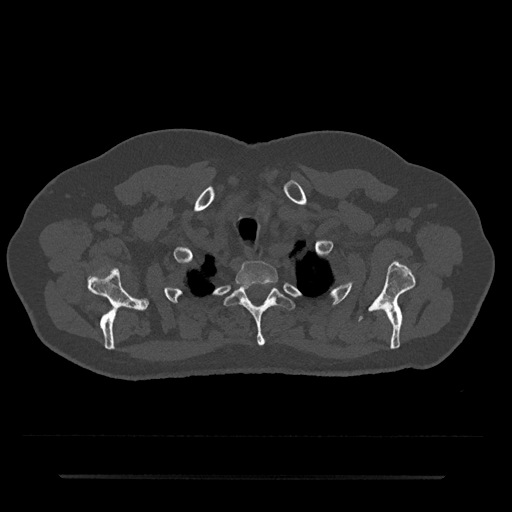
CT including the spine, one axial slice; slice 615 of 797 in the series (ordered by position); reconstruction kernel Br40s/3; 120 kVp; bone window (W 1800 / L 400 HU); 512 × 512 image matrix. Patient: male, 69 years. From the clinical record (not read from this slice): primary cancer: prostate.
Structures marked on this image (semi-automatic segmentation, software-assisted and operator-edited):
- T1 vertebra: bounding box [x1, y1, x2, y2] px = [235, 260, 278, 286]
- T2 vertebra: [225, 281, 295, 346]